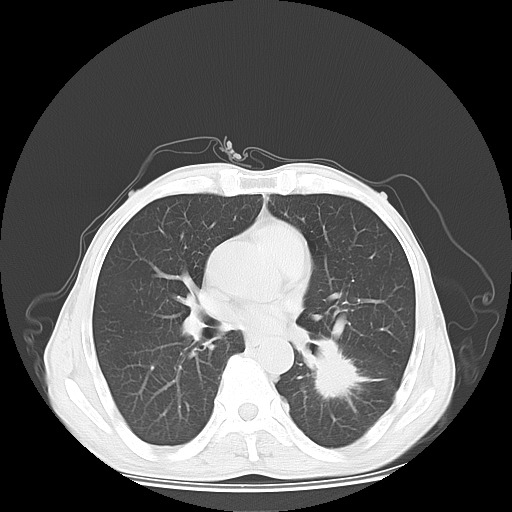
Chest CT, one axial slice; position 33 of 65 along the scan axis; 120 kVp; lung window (W 1500 / L -600 HU); 5 mm slice thickness; 512 × 512 image matrix, field of view 350 × 350 mm. Male patient, age 63 years. Case-level facts recorded for this patient, not image findings: clinical TNM (as recorded): T1c N0 M1b.
Outlined on this slice (rectangle marked by the reading radiologist):
- lung tumour (recorded histology: adenocarcinoma): bounding box (x1, y1, x2, y2) in pixels: (304, 338, 370, 412)